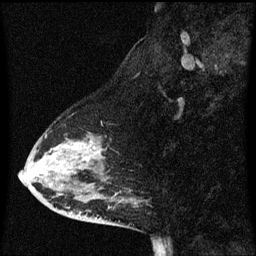
Breast MRI (dynamic contrast-enhanced), one sagittal slice; position 25 of 60 along the scan axis; dynamic contrast-enhanced series, image 2 of 3 at this slice position (ordered by acquisition); 1.5 T; TE 4.2 ms, TR 8.4 ms; 256 × 256 image matrix. Patient: female, 47 years. From the clinical record (not read from this slice): setting: breast cancer imaged before/during neoadjuvant chemotherapy; receptor status: HER2-positive.
Structures marked on this image (semi-automatically segmented with operator editing):
- analysis volume of interest (the breast-tissue region the enhancement analysis was run in; not a lesion): bounding box (x1, y1, x2, y2) in pixels: (26, 128, 137, 201)
- tumour enhancement mask (voxels above the 70 % enhancement threshold inside the analysis volume of interest): (72, 144, 85, 149)